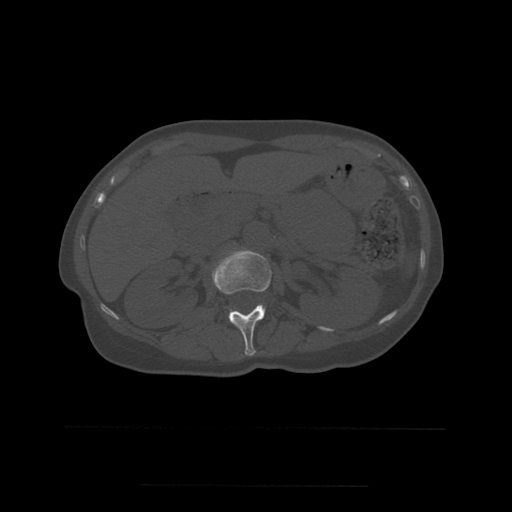
CT including the spine, one axial slice; slice 229 of 544 in the series (ordered by position); bone window (W 1800 / L 400 HU); 1.25 mm slice thickness; 512 × 512 image matrix. Patient age 58 years. Case-level facts recorded for this patient, not image findings: primary cancer: lung.
Outlined on this slice (semi-automatic segmentation, software-assisted and operator-edited):
- L1 vertebra: bounding box (x1, y1, x2, y2) in pixels: (212, 250, 272, 356)